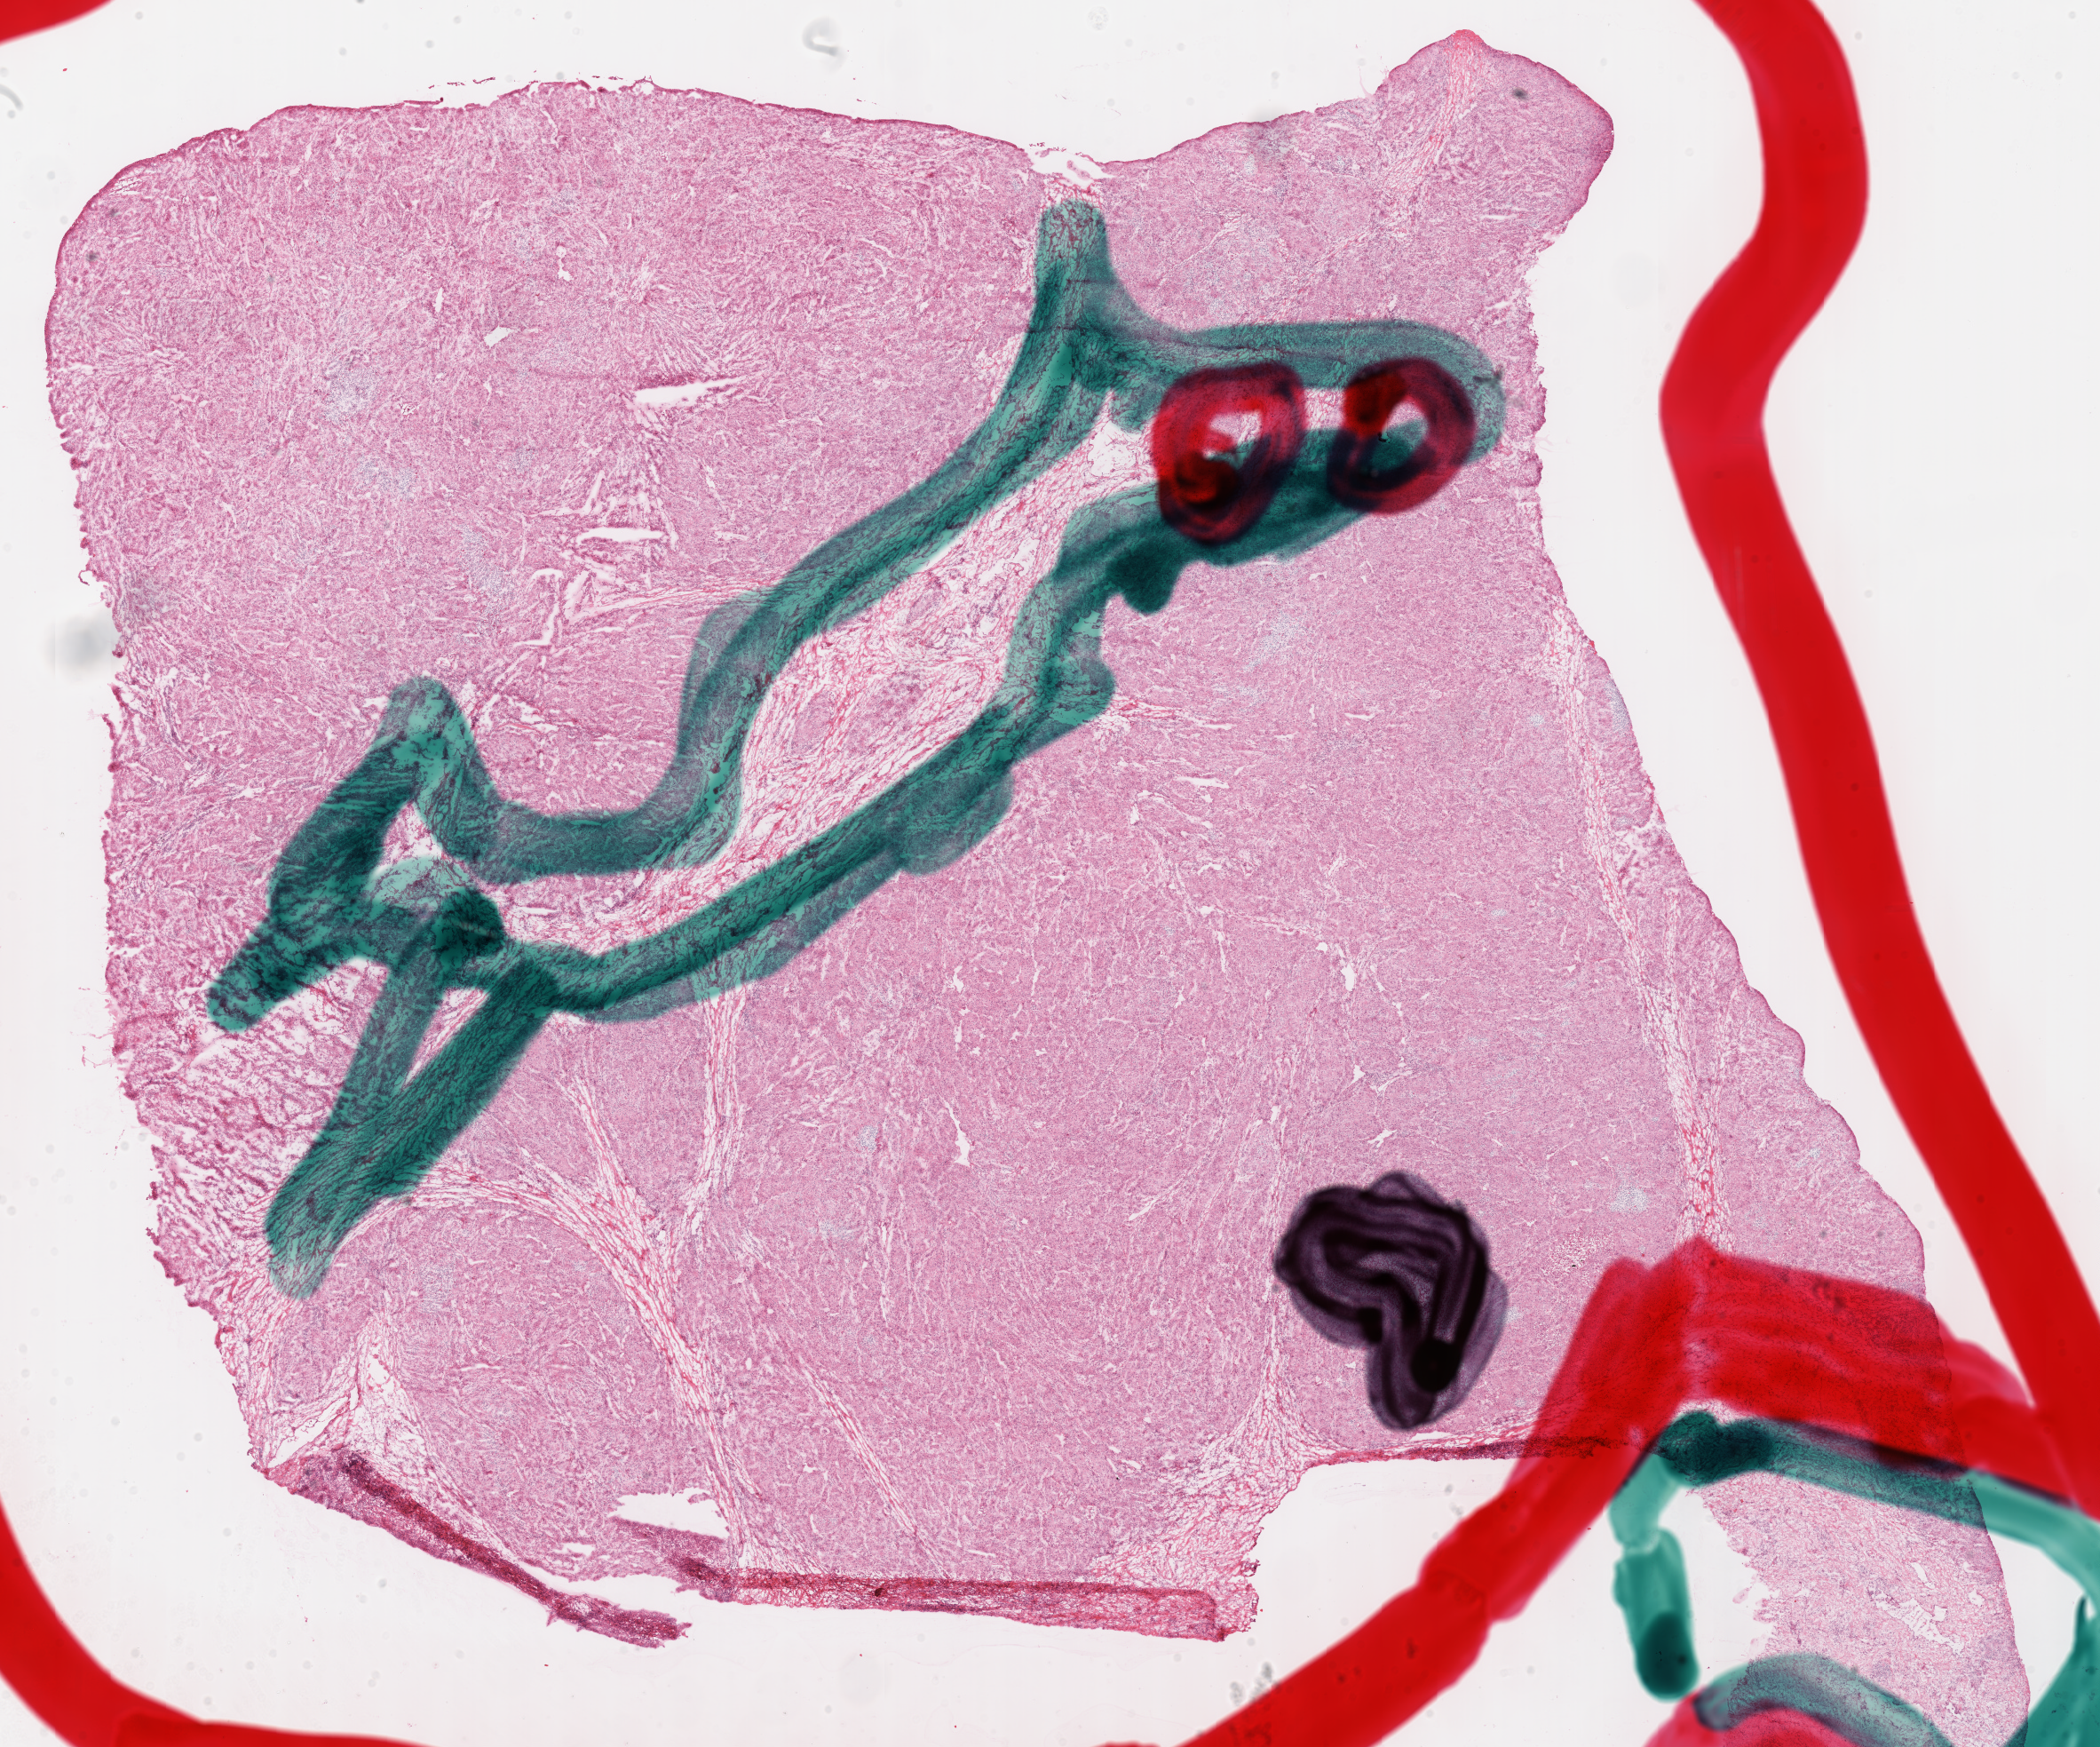
H&E whole-slide image, low-resolution overview of the scanned area, about 18.6 x 15.5 mm (from a 40x scan). Frozen section from the top of the tissue portion. Sample: primary tumour, lung. Patient: male, age at initial diagnosis 70 years. Pathologist review of this section (percent, as recorded): tumour cells 100%, tumour nuclei 70%, normal cells 0%, stromal cells 0%, necrosis 0%. Infiltration values recorded for this section: lymphocyte infiltration 8%, monocyte infiltration 0%, neutrophil infiltration 18%.
Histologic diagnosis: Adenocarcinoma, NOS. AJCC pathologic stage: IIA.